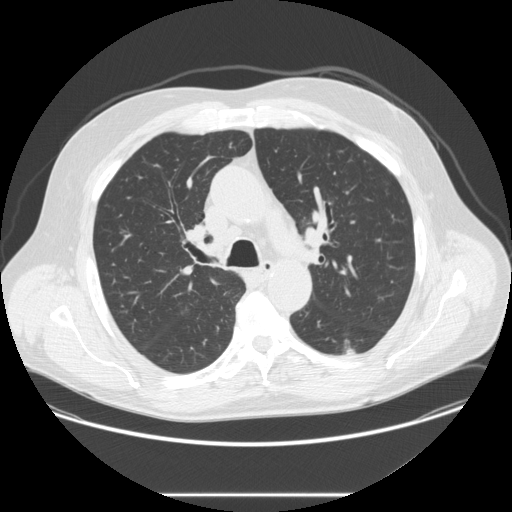
Low-dose screening chest CT, one axial slice; reconstruction kernel STANDARD; lung window (W 1500 / L -600 HU); 2.5 mm slice thickness; 512 × 512 image matrix, field of view 420 × 420 mm.
Annotated regions visible in this slice (outlined manually by an expert reader):
- lesion 1 (tumor, lower lobe of left lung): bounding box (x1, y1, x2, y2) in pixels: (345, 346, 356, 355)